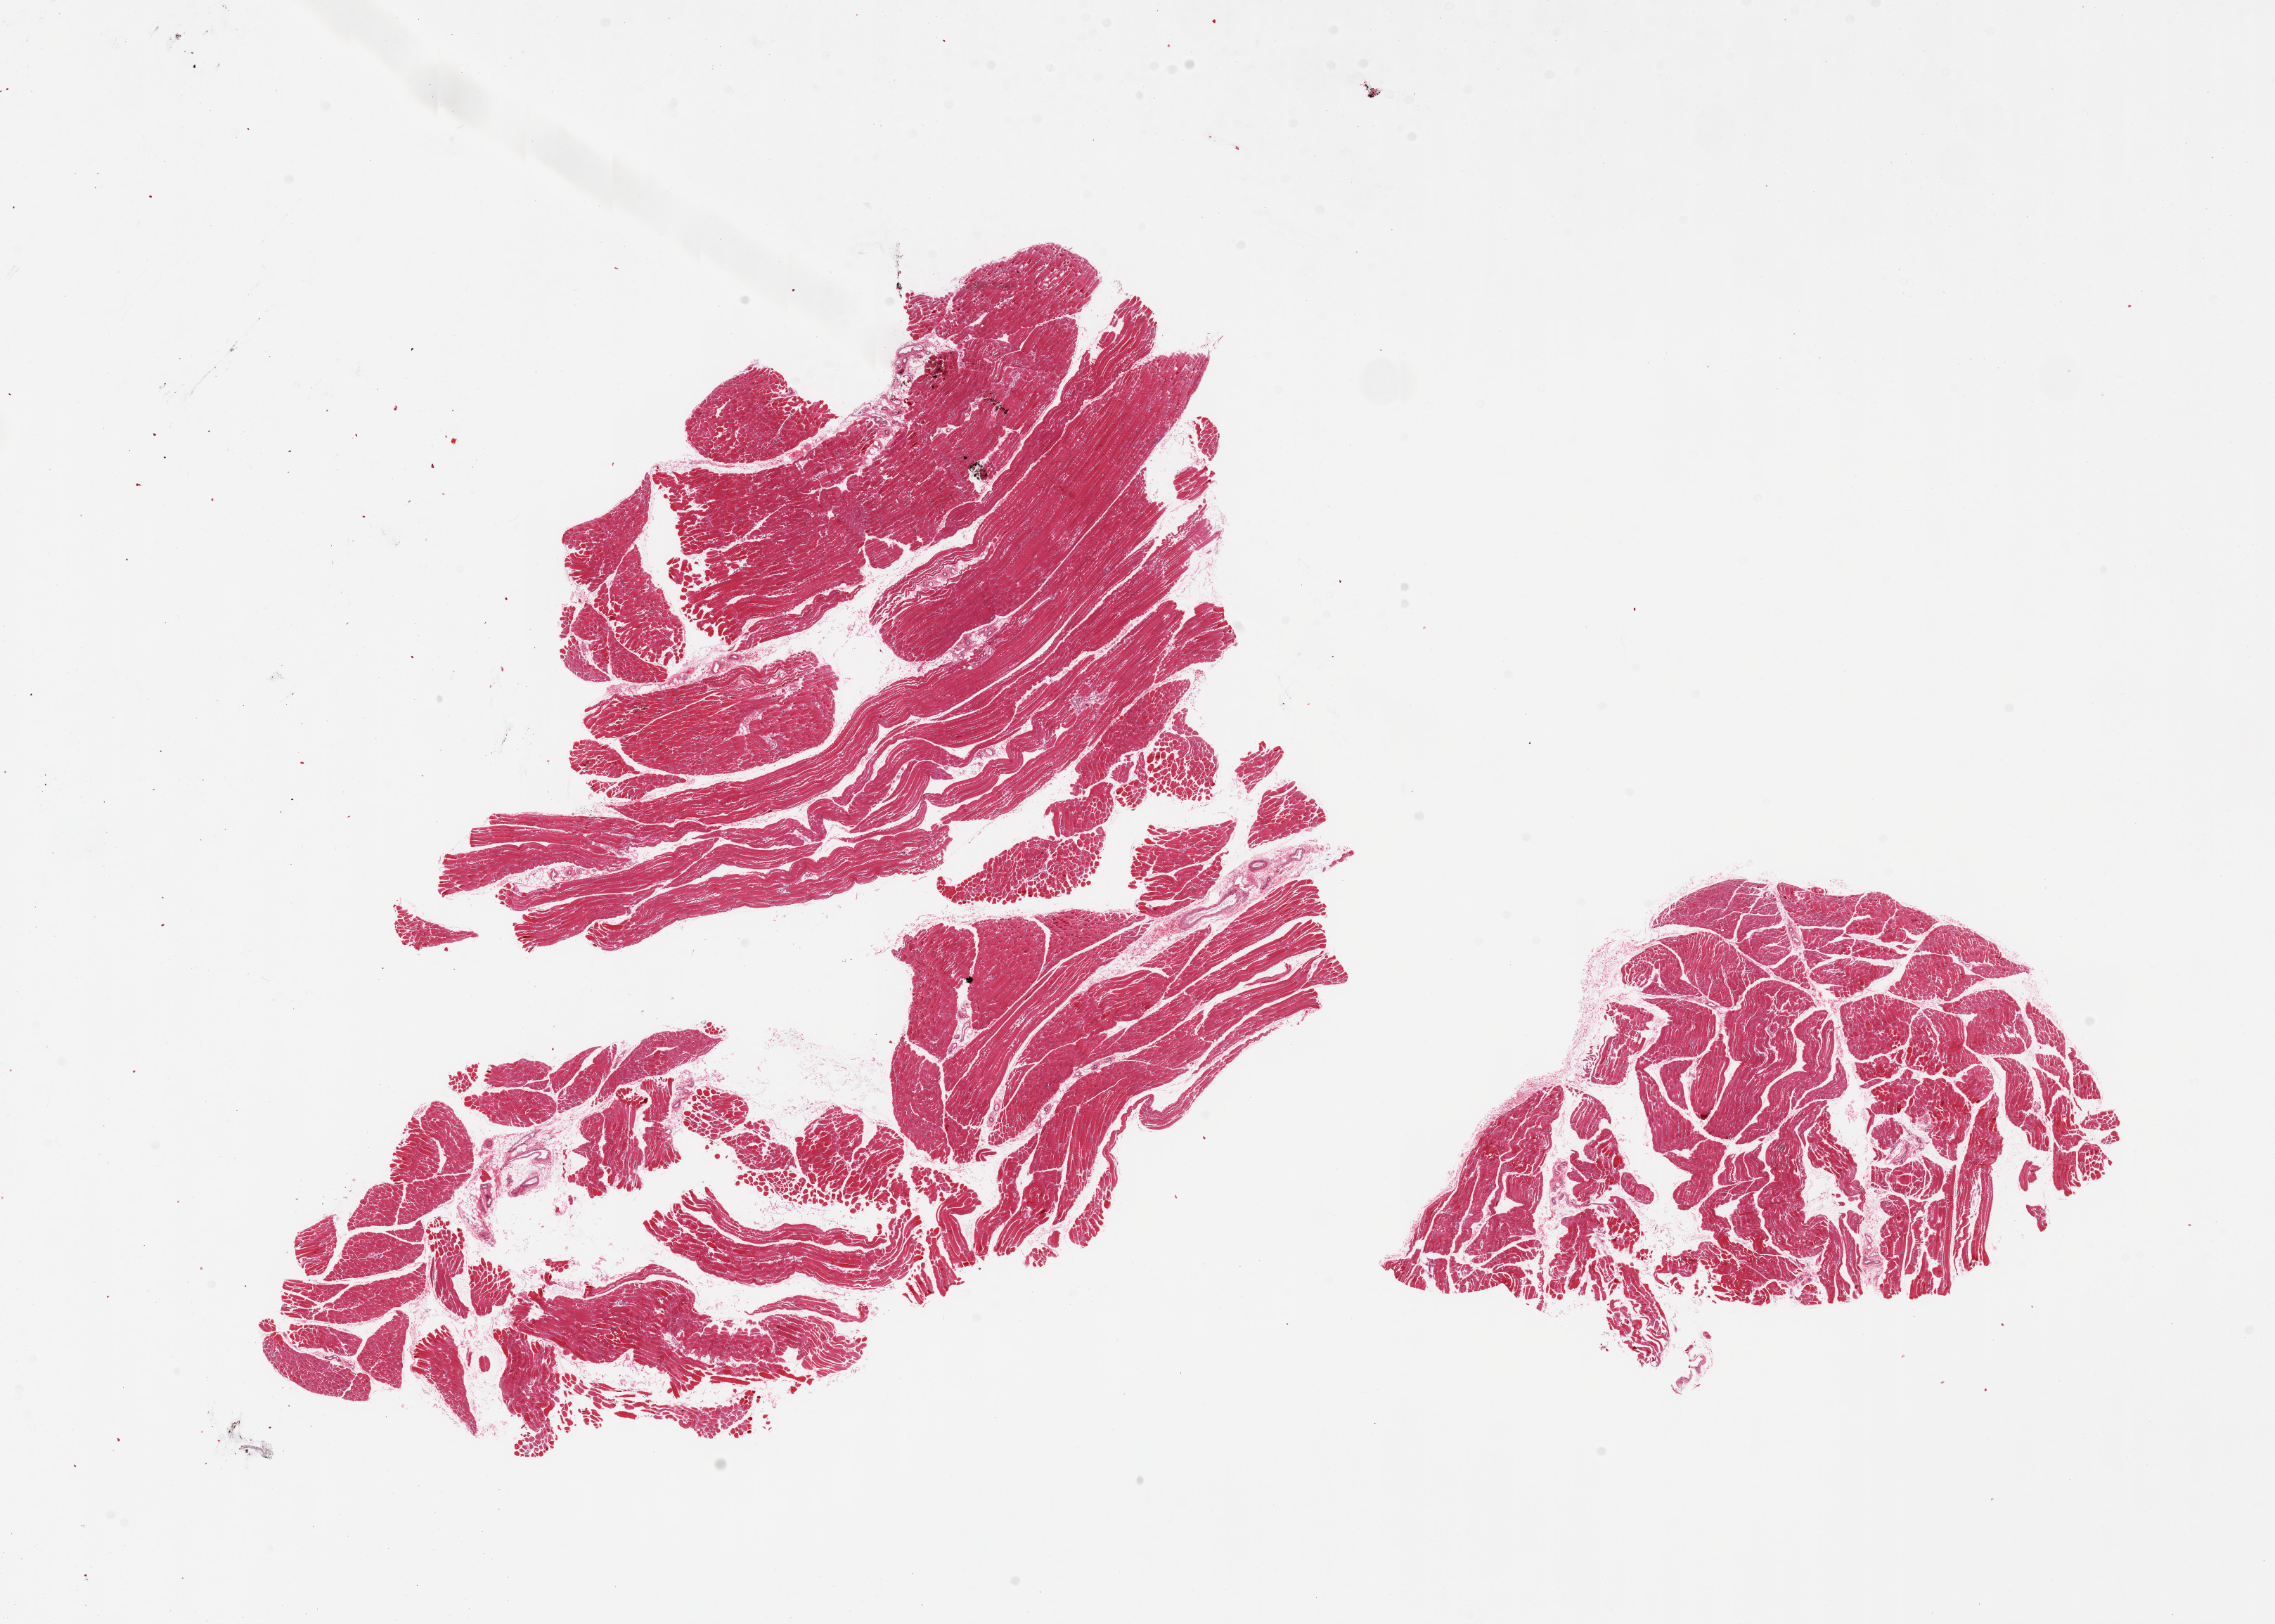
Haematoxylin and eosin whole-slide image — low-resolution overview of the scanned area, about 25.6 x 18.3 mm; PAXgene-fixed paraffin-embedded (PFPE) section; section of skeletal muscle (target tissue); donor tissue sample. Donor: female.
* reviewer comment on this tissue sample: 2 pieces